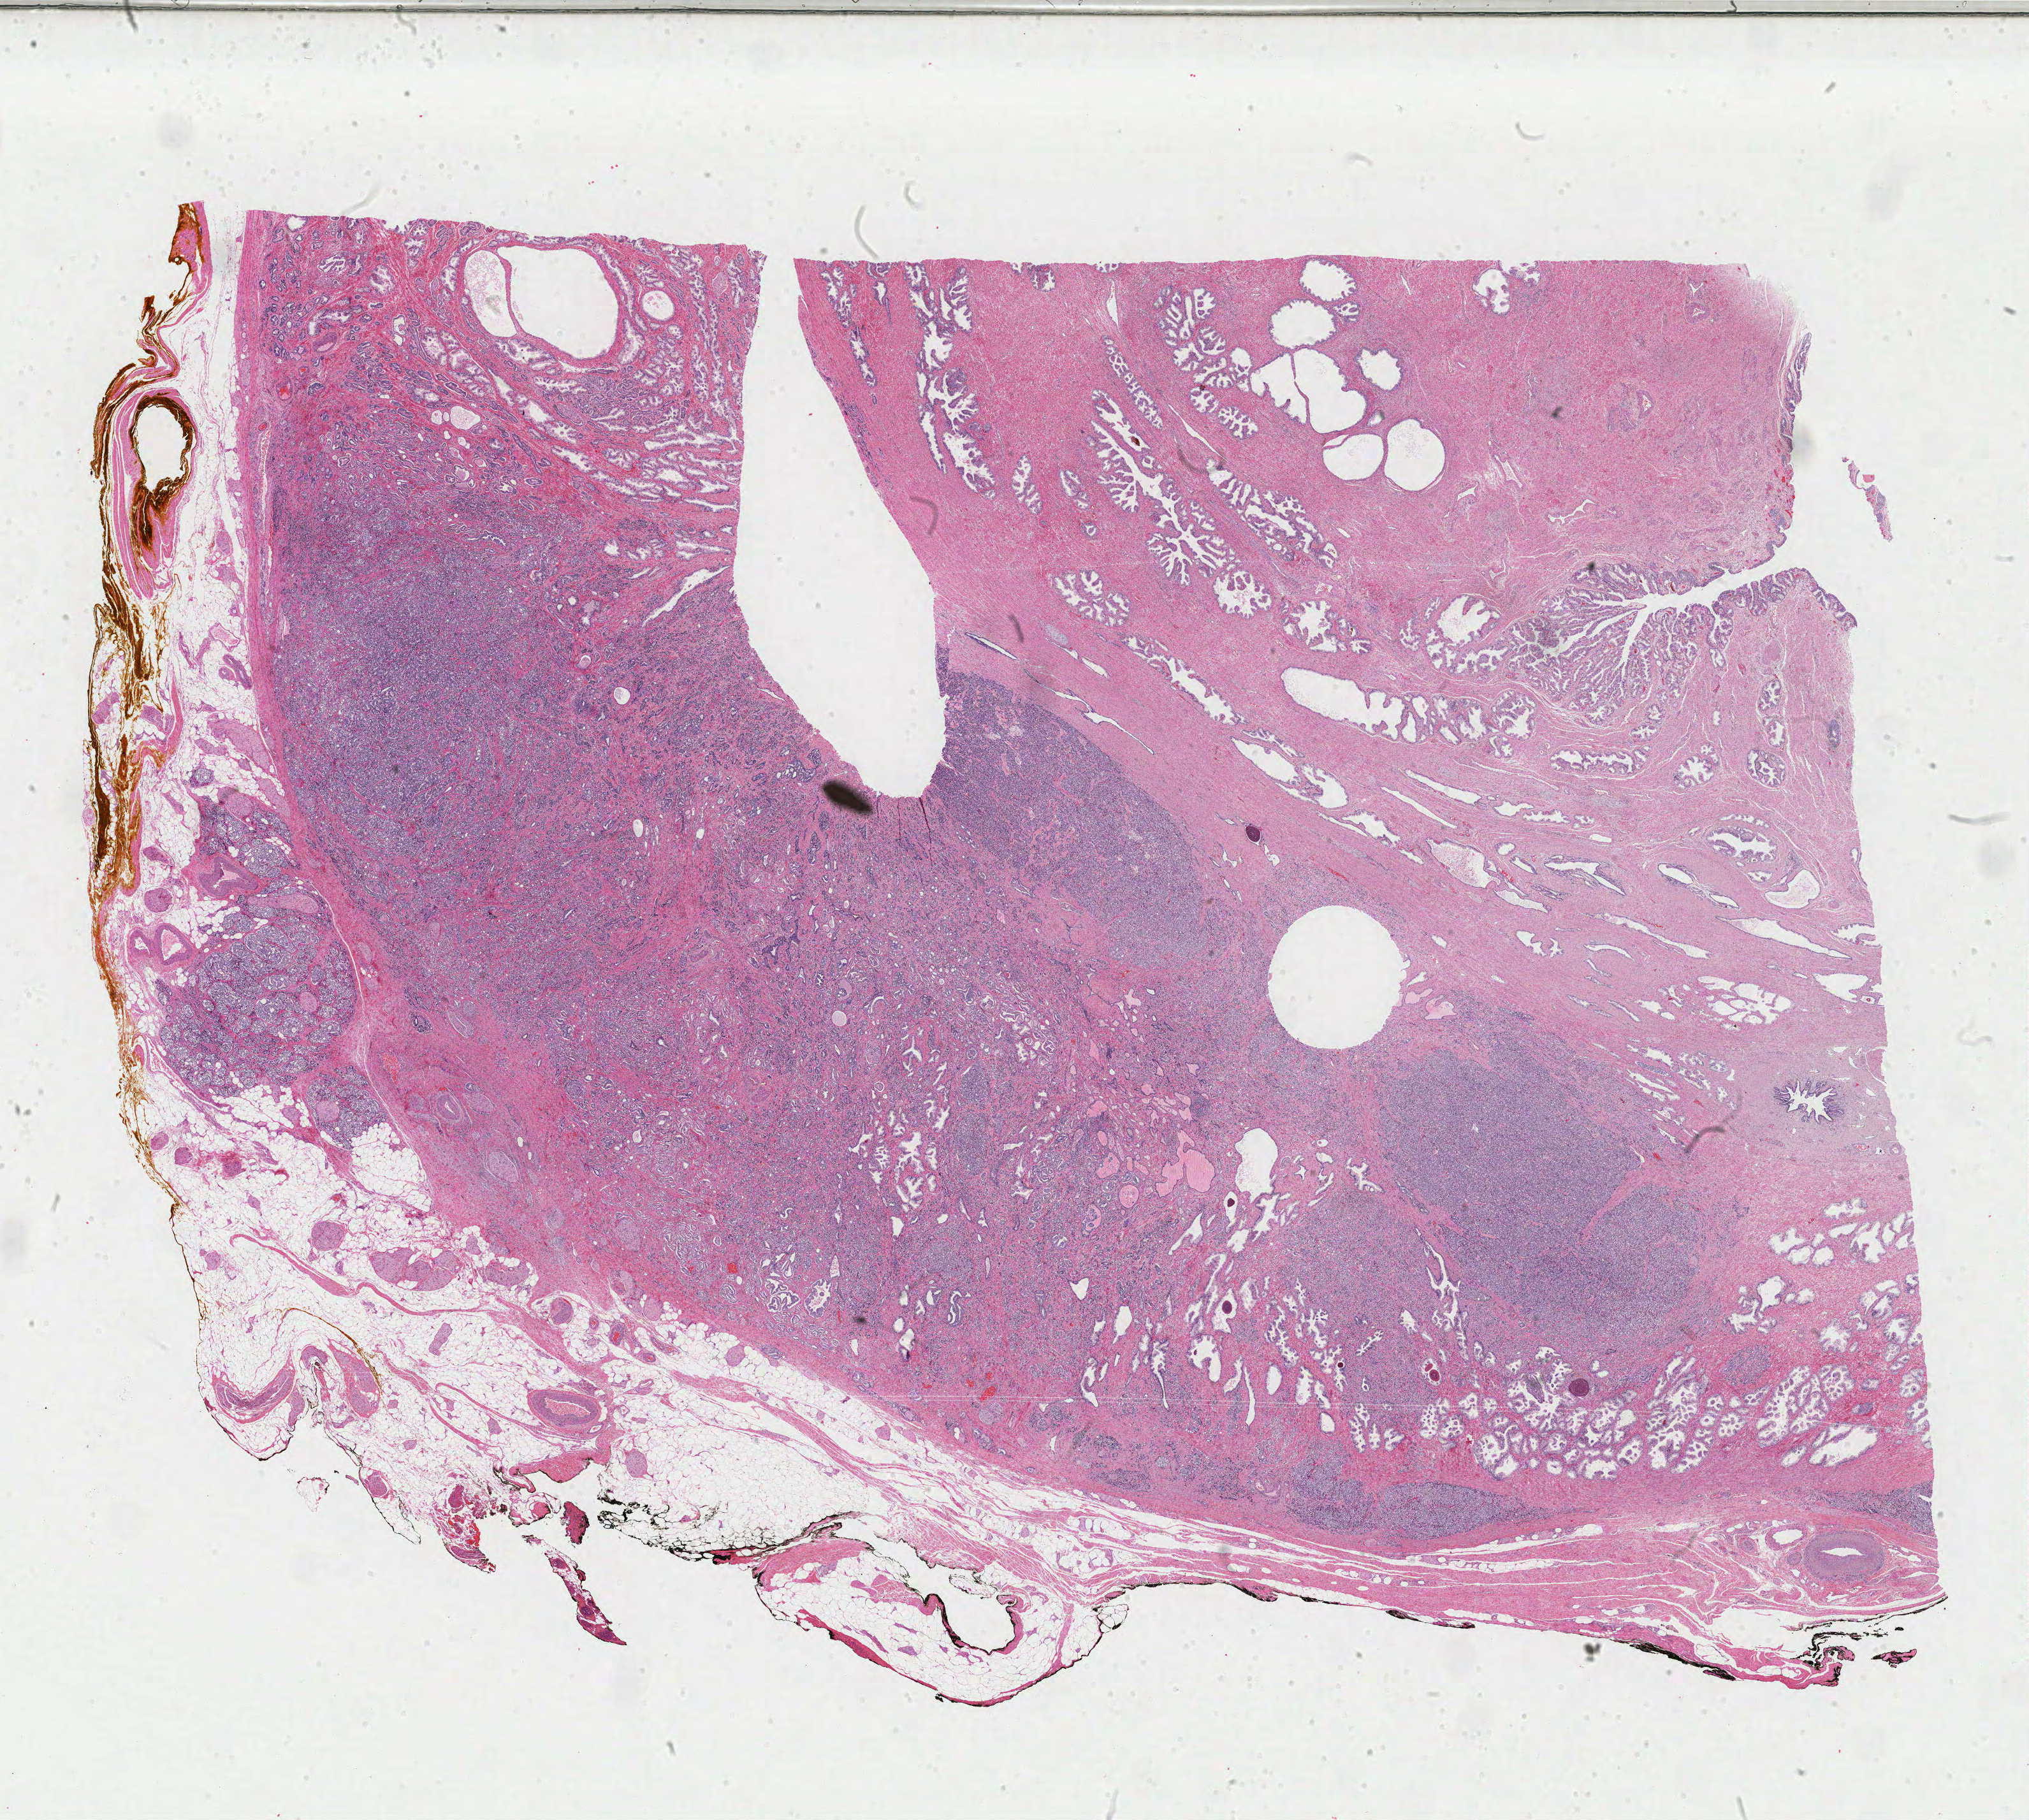
H&E-stained whole-slide image — whole scanned area (about 25.3 x 22.7 mm, from a 40x scan) shown as a low-resolution overview; formalin-fixed paraffin-embedded (FFPE) diagnostic section; sample: primary tumour, prostate. Male, age 55 years at initial diagnosis.
Pathologic diagnosis: Adenocarcinoma, NOS.